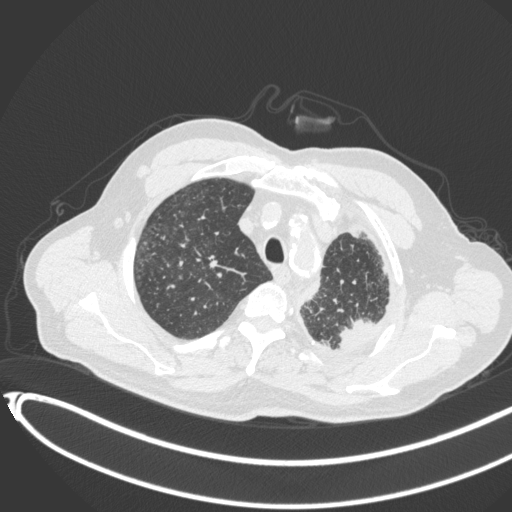
Chest CT, one axial slice. Position 355 of 451 along the scan axis. Reconstruction kernel B31f. Lung window (W 1500 / L -600 HU). 512 × 512 image matrix, field of view 400 × 400 mm. Male patient, age 78 years. Case-level facts recorded for this patient, not image findings: clinical TNM (as recorded): T1c N0 M1.
Annotated regions visible in this slice (bounding box drawn by a radiologist):
- lung tumour (recorded histology: adenocarcinoma): bounding box [x1, y1, x2, y2] px = [337, 314, 384, 359]